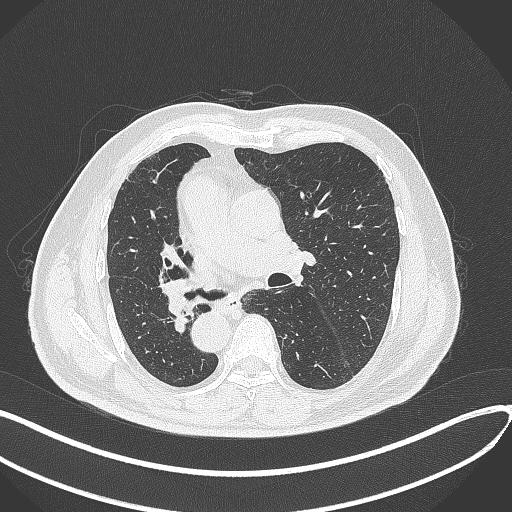
Chest CT, one axial slice. Reconstruction kernel B70f. 120 kVp. Lung window (W 1500 / L -600 HU). 1 mm slice thickness. 512 × 512 image matrix. Male patient, age 67 years. From the clinical record (not read from this slice): clinical TNM (as recorded): T2a N0 M0.
Structures marked on this image (bounding box drawn by a radiologist):
- lung tumour (recorded histology: squamous cell carcinoma): bounding box <156,275,189,316> (left, top, right, bottom; pixels)